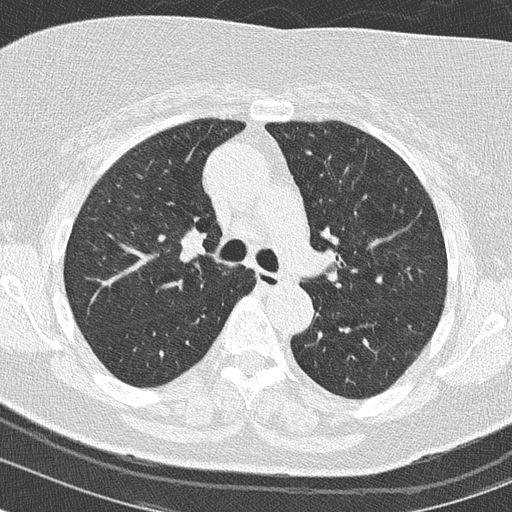
Low-dose screening chest CT, axial slice; baseline screening round; lung window (W 1500 / L -600 HU); 2 mm slice thickness; lung (sharp) reconstruction kernel (B50f); slice 47 of 149 in the series. Female, age 63 years at enrolment.
- Lesion marked by an expert reader, bounding box (x1, y1, x2, y2) in pixels: (167, 219, 229, 274).
- Screening reader's record for this exam: no non-calcified nodule ≥4 mm recorded.
- Lung cancer was diagnosed 149 days after this screen: squamous cell carcinoma, keratinizing, NOS, right upper lobe, moderately differentiated (G2), stage IIA (AJCC 6th edition), 42 mm at pathology.